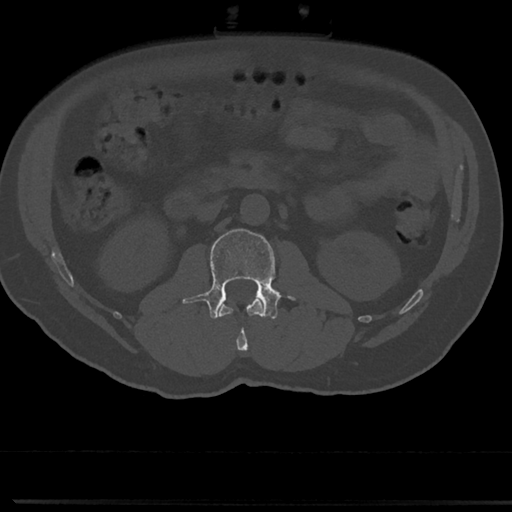
CT including the spine, one axial slice; slice 32 of 817 in the series (ordered by position); 120 kVp; bone window (W 1800 / L 400 HU); 512 × 512 image matrix. Male patient, age 61 years. Case-level facts recorded for this patient, not image findings: primary cancer: prostate.
Structures marked on this image (semi-automatic segmentation, software-assisted and operator-edited):
- L1 vertebra: box from (x=219, y=298) to (x=263, y=352) px
- L2 vertebra: (x=191, y=228)–(x=293, y=319)